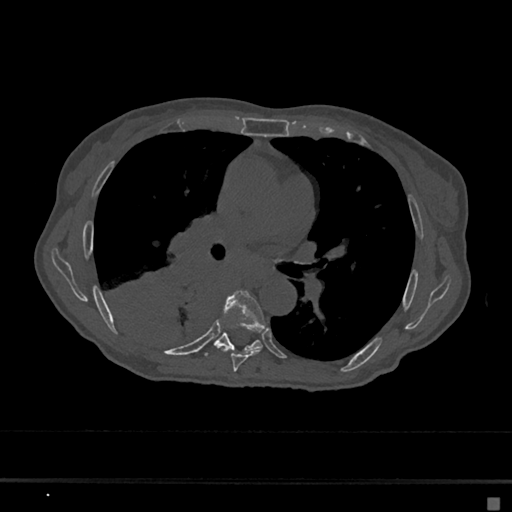
CT including the spine, one axial slice. Slice 398 of 797 in the series (ordered by position). 120 kVp. Bone window (W 1800 / L 400 HU). 512 × 512 image matrix, field of view 360 × 360 mm. Patient: female, 68 years. Case-level facts recorded for this patient, not image findings: primary cancer: renal.
Structures marked on this image (semi-automatic segmentation, software-assisted and operator-edited):
- T6 vertebra: box from (x=222, y=290) to (x=266, y=372) px
- T7 vertebra: (x=204, y=331)–(x=263, y=356)